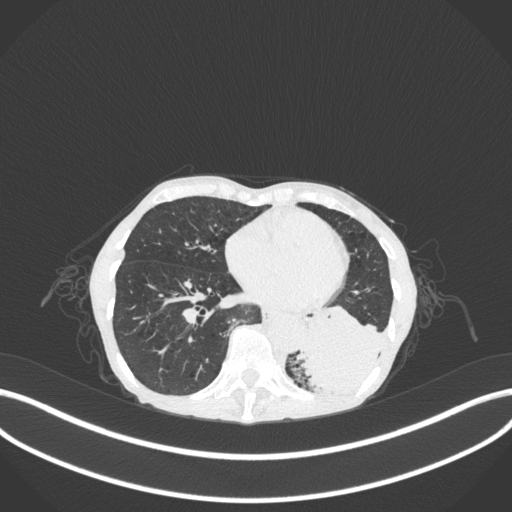
Chest CT, one axial slice. Position 91 of 347 along the scan axis. Reconstruction kernel B31f. 120 kVp. Lung window (W 1500 / L -600 HU). 1 mm slice thickness. 512 × 512 image matrix, field of view 400 × 400 mm. Female patient, age 70 years. Case-level facts recorded for this patient, not image findings: clinical TNM (as recorded): T3 N0 M0.
Outlined on this slice (rectangle marked by the reading radiologist):
- lung tumour (recorded histology: small cell carcinoma): bounding box <298,302,396,396> (left, top, right, bottom; pixels)